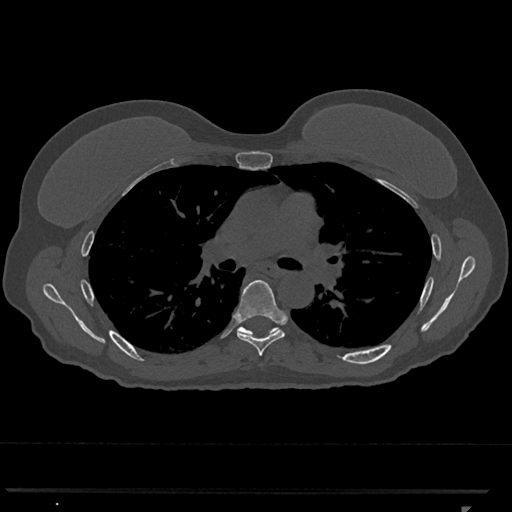
CT including the spine, one axial slice; position 752 of 793 along the scan axis; reconstruction kernel Br40s/3; bone window (W 1800 / L 400 HU); 0.5 mm slice thickness; 512 × 512 image matrix, field of view 380 × 380 mm. Patient: female, 62 years. From the clinical record (not read from this slice): primary cancer: renal.
Annotated regions visible in this slice (semi-automatic segmentation, software-assisted and operator-edited):
- T6 vertebra: bounding box [x1, y1, x2, y2] px = [234, 279, 285, 356]
- T7 vertebra: [237, 326, 278, 336]